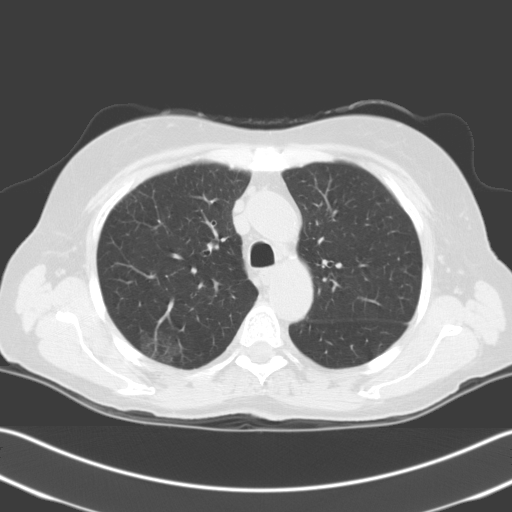
Axial slice from a low-dose chest CT screening exam. First (baseline) screen. Lung window (W 1500 / L -600 HU). 3.2 mm slice thickness. Standard (soft-tissue) reconstruction kernel (C). Female, age 67 years at enrolment. Current smoker at enrolment.
- Lesion marked by an expert reader, bounding box [x1, y1, x2, y2] px = [126, 324, 188, 373].
- The screening reader recorded 2 non-calcified nodules or masses ≥4 mm on this exam; which of them this box marks is not recorded.
- Official screen result: positive, change unspecified: nodule(s) >= 4 mm or enlarging nodule(s), mass(es), or other non-specific abnormalities suspicious for lung cancer.
- Lung cancer was diagnosed 24 days after this screen: squamous cell carcinoma, NOS, right upper lobe, stage IIIA (AJCC 6th edition), 56 mm at pathology.